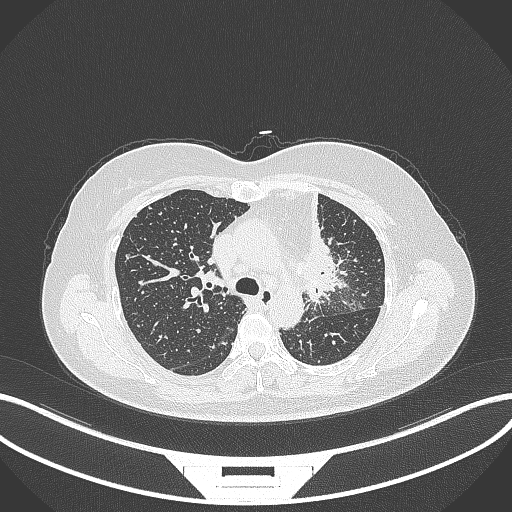
Chest CT, one axial slice. Position 227 of 348 along the scan axis. Reconstruction kernel B70f. 120 kVp. Lung window (W 1500 / L -600 HU). 1 mm slice thickness. 512 × 512 image matrix, field of view 400 × 400 mm. Female patient, age 49 years. Case-level facts recorded for this patient, not image findings: clinical TNM (as recorded): T1c N0 M1.
Outlined on this slice (rectangle marked by the reading radiologist):
- lung tumour (recorded histology: adenocarcinoma): bounding box <291,190,342,308> (left, top, right, bottom; pixels)